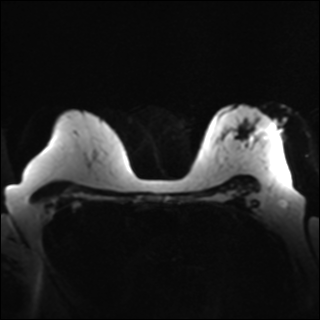
Breast MRI, one axial slice; slice 21 of 35 in the series (ordered by position); diffusion-weighted series; image 2 of 4 stored at this slice position (different b-values; order by instance number); 1.5 T; 320 × 320 image matrix, field of view 320 × 320 mm. Female patient.
Outlined on this slice (outlined manually by an expert reader):
- tumour on diffusion-weighted imaging: box from (x=267, y=124) to (x=276, y=139) px